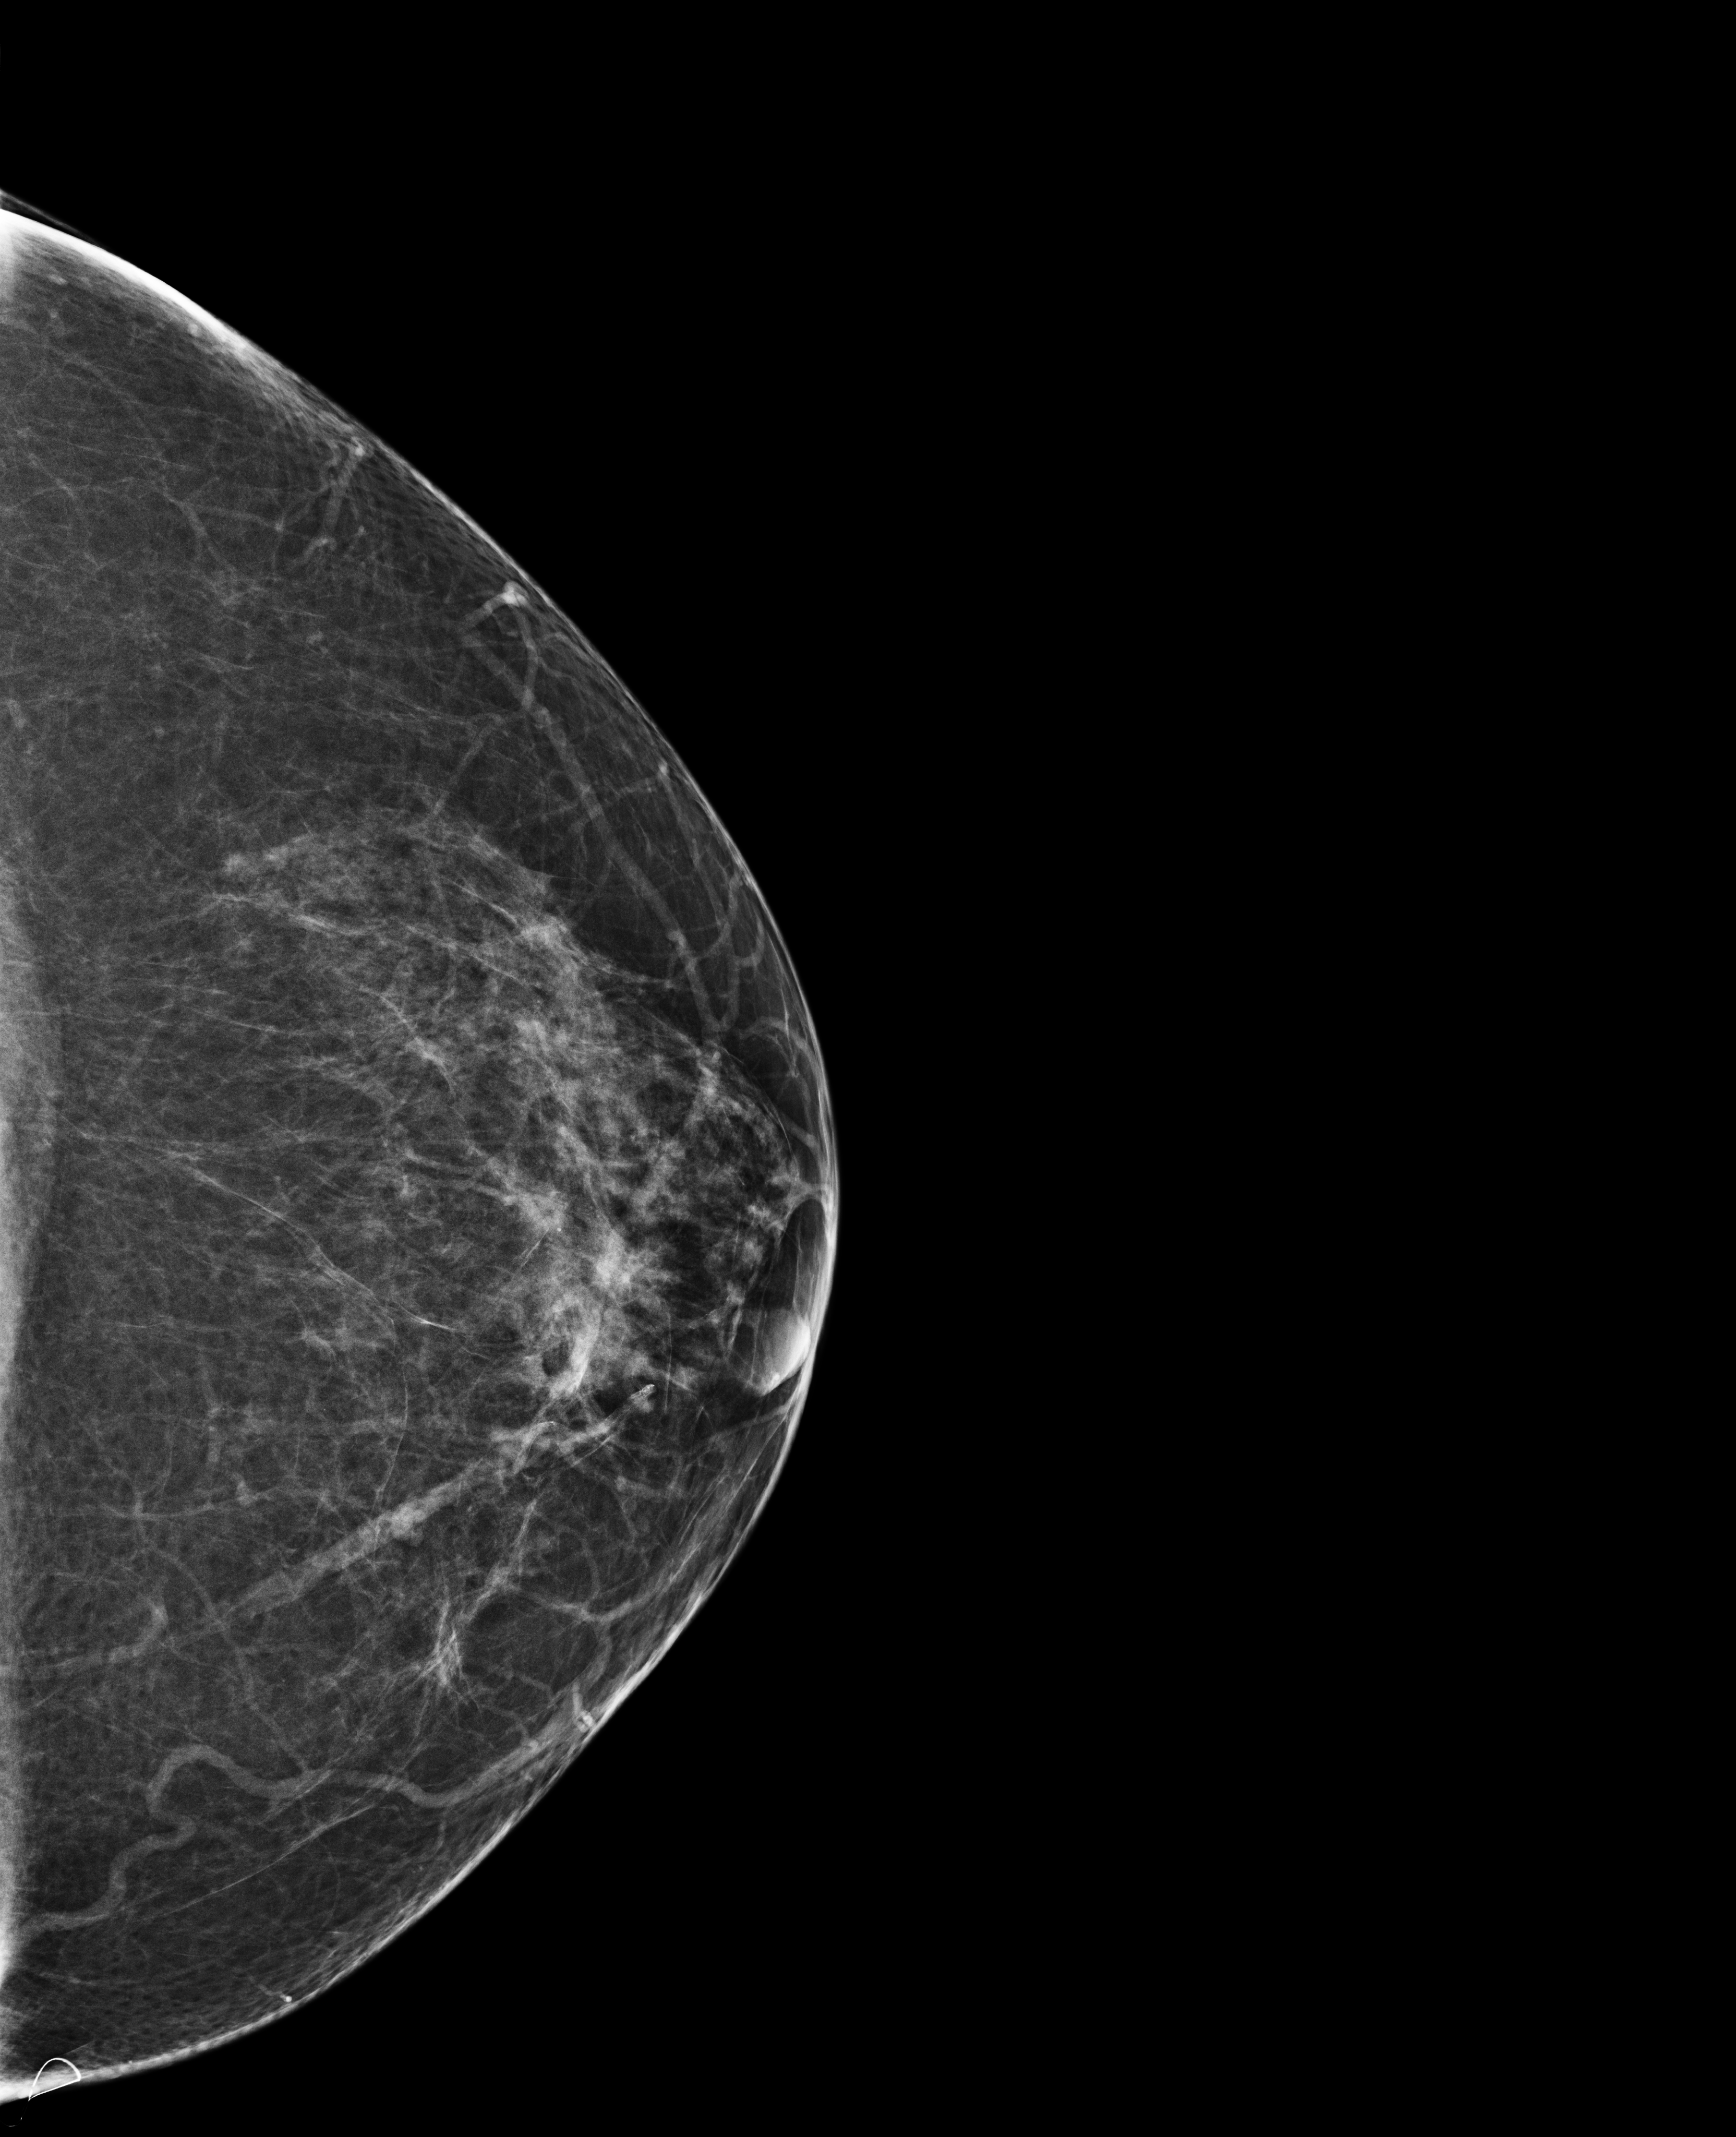
Digital mammogram (FFDM); left breast; cranio-caudal projection; screening examination; compressed breast thickness 70 mm; system: Selenia Dimensions. Female patient, age 61 years.
- breast density at the screening exam (both breasts): heterogeneously dense (BI-RADS density category c)
- final BI-RADS assessment for this screening round (tomosynthesis exam, both breasts): category 1
- recall: no recall after this screen